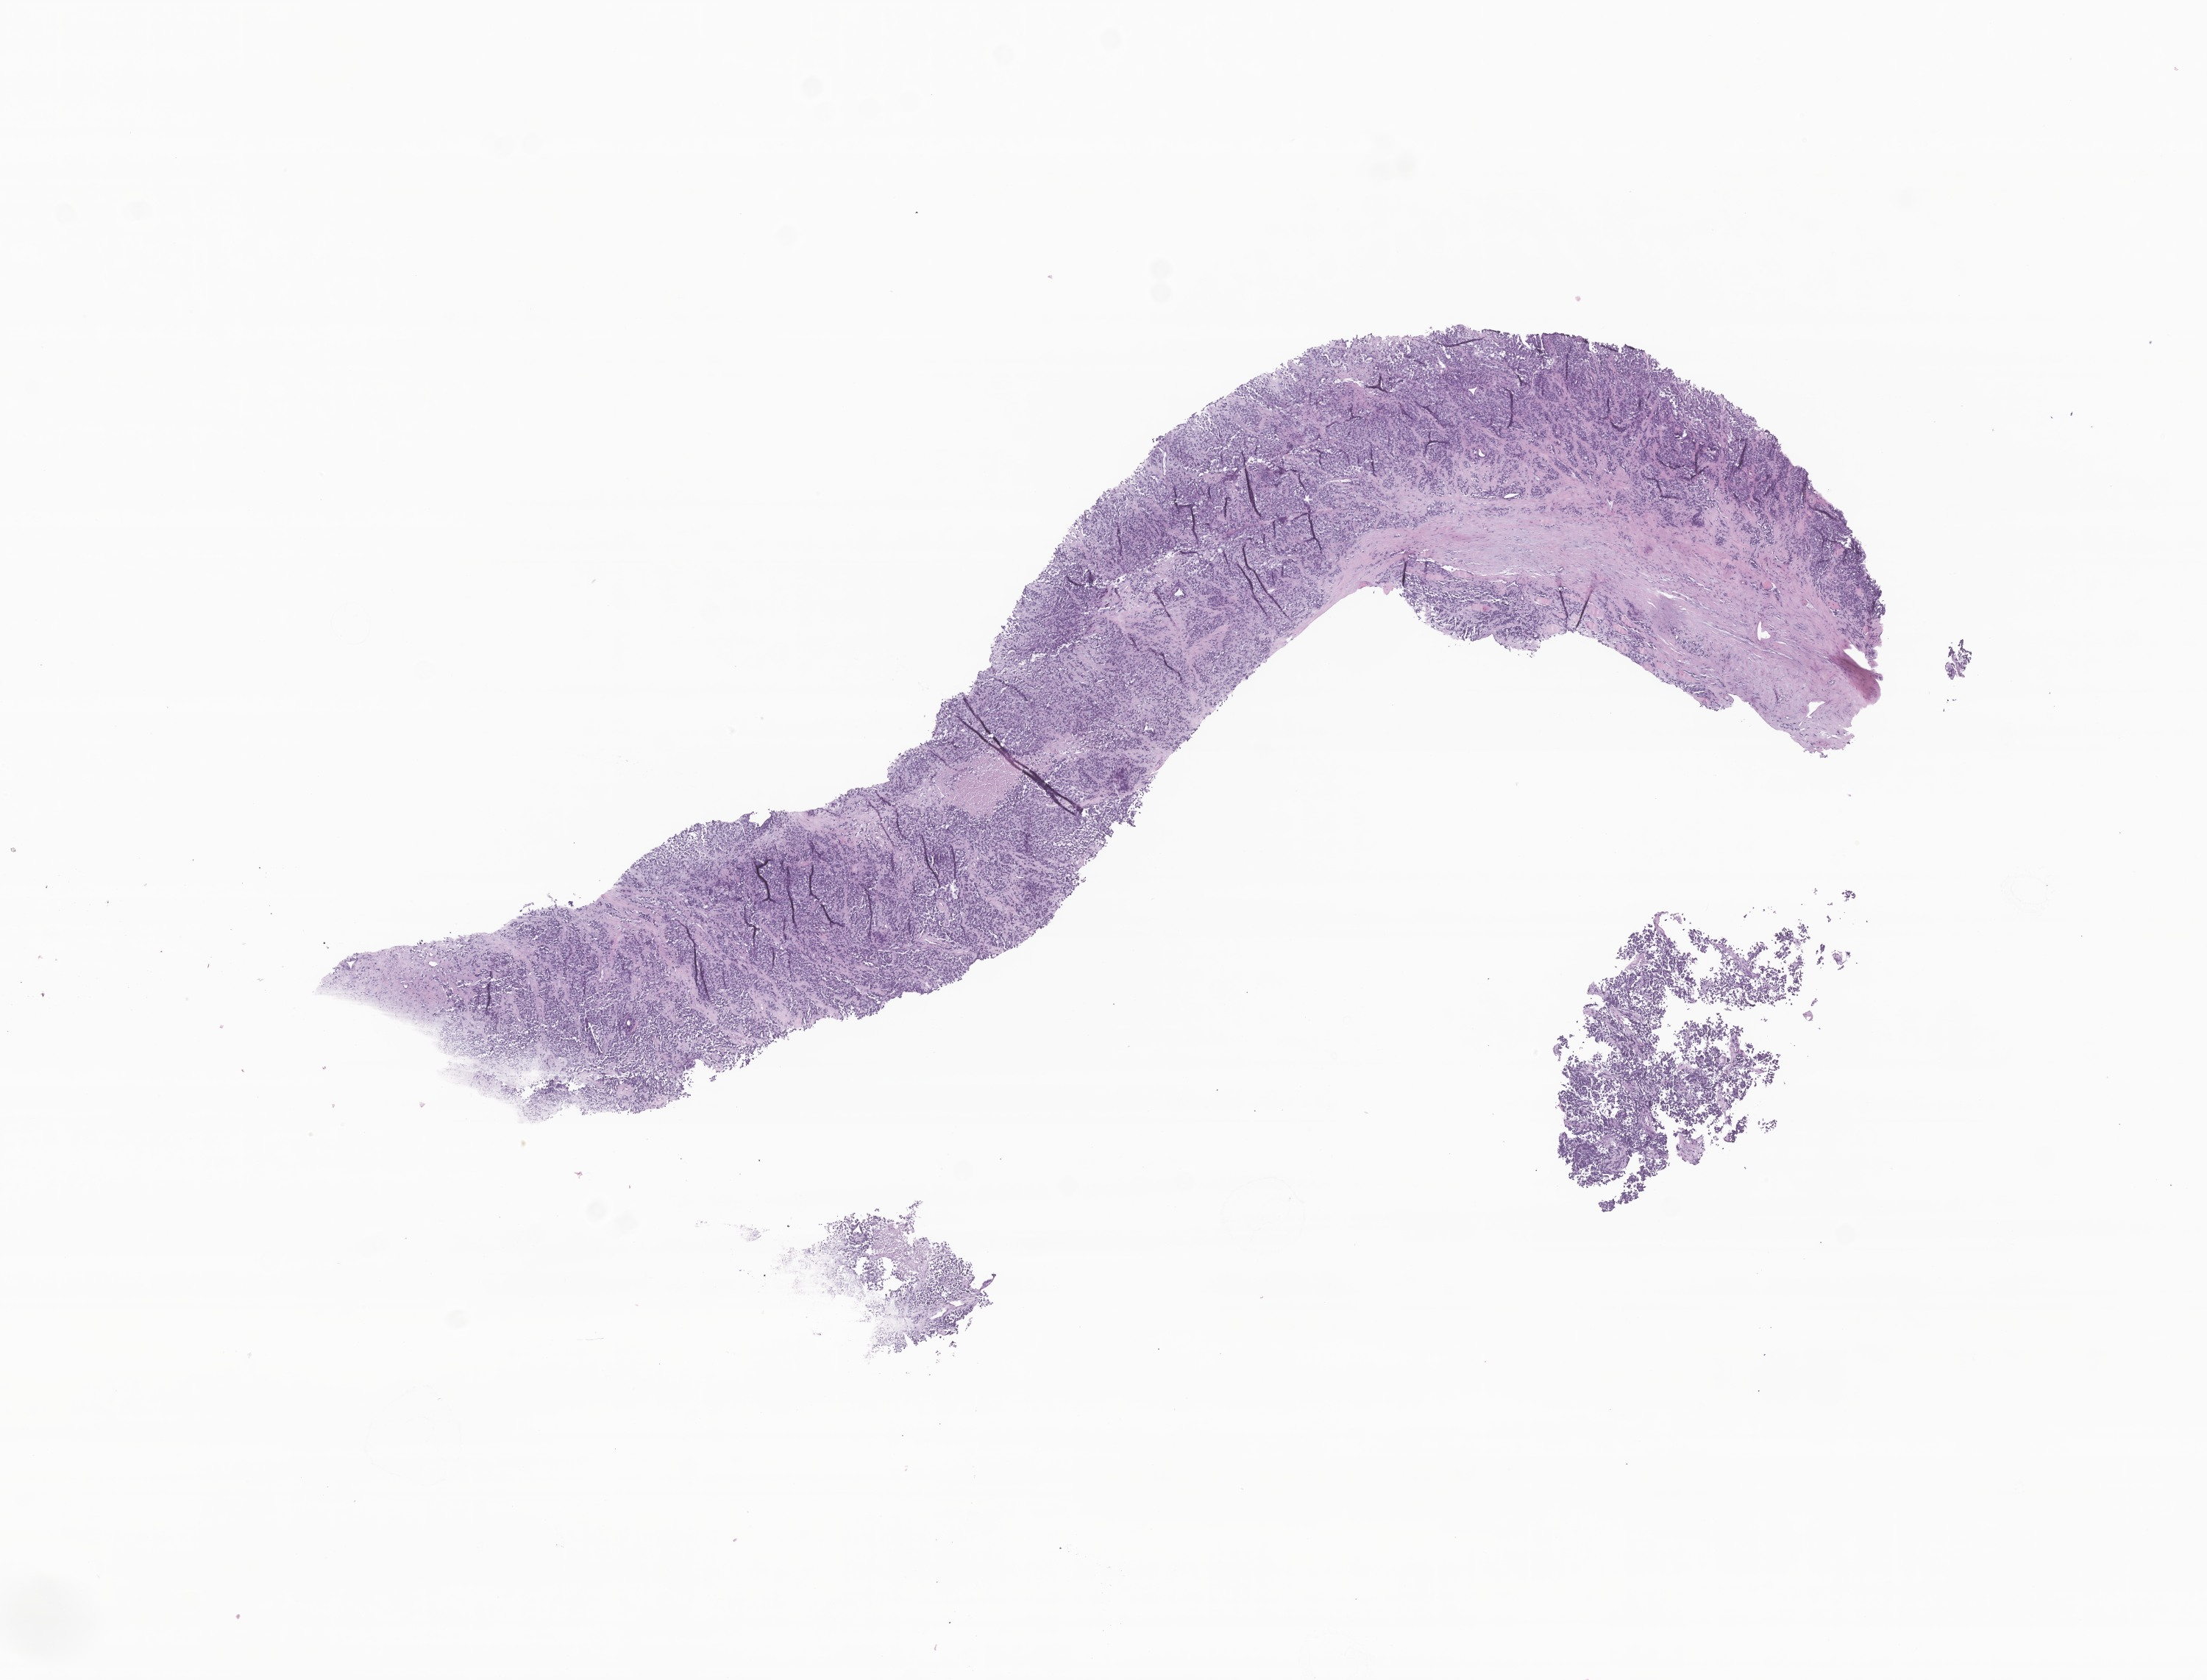
Whole-slide image, H&E stain of tumor tissue from the soft tissue of lower extremity — low-resolution overview of the scanned area, about 12.6 x 9.6 mm; formalin-fixed paraffin-embedded section. Patient female; age 130 months (10 years 10 months).
- tissue or organ of origin (case record): connective, subcutaneous and other soft tissues of lower limb and hip
- recorded diagnosis: Alveolar rhabdomyosarcoma